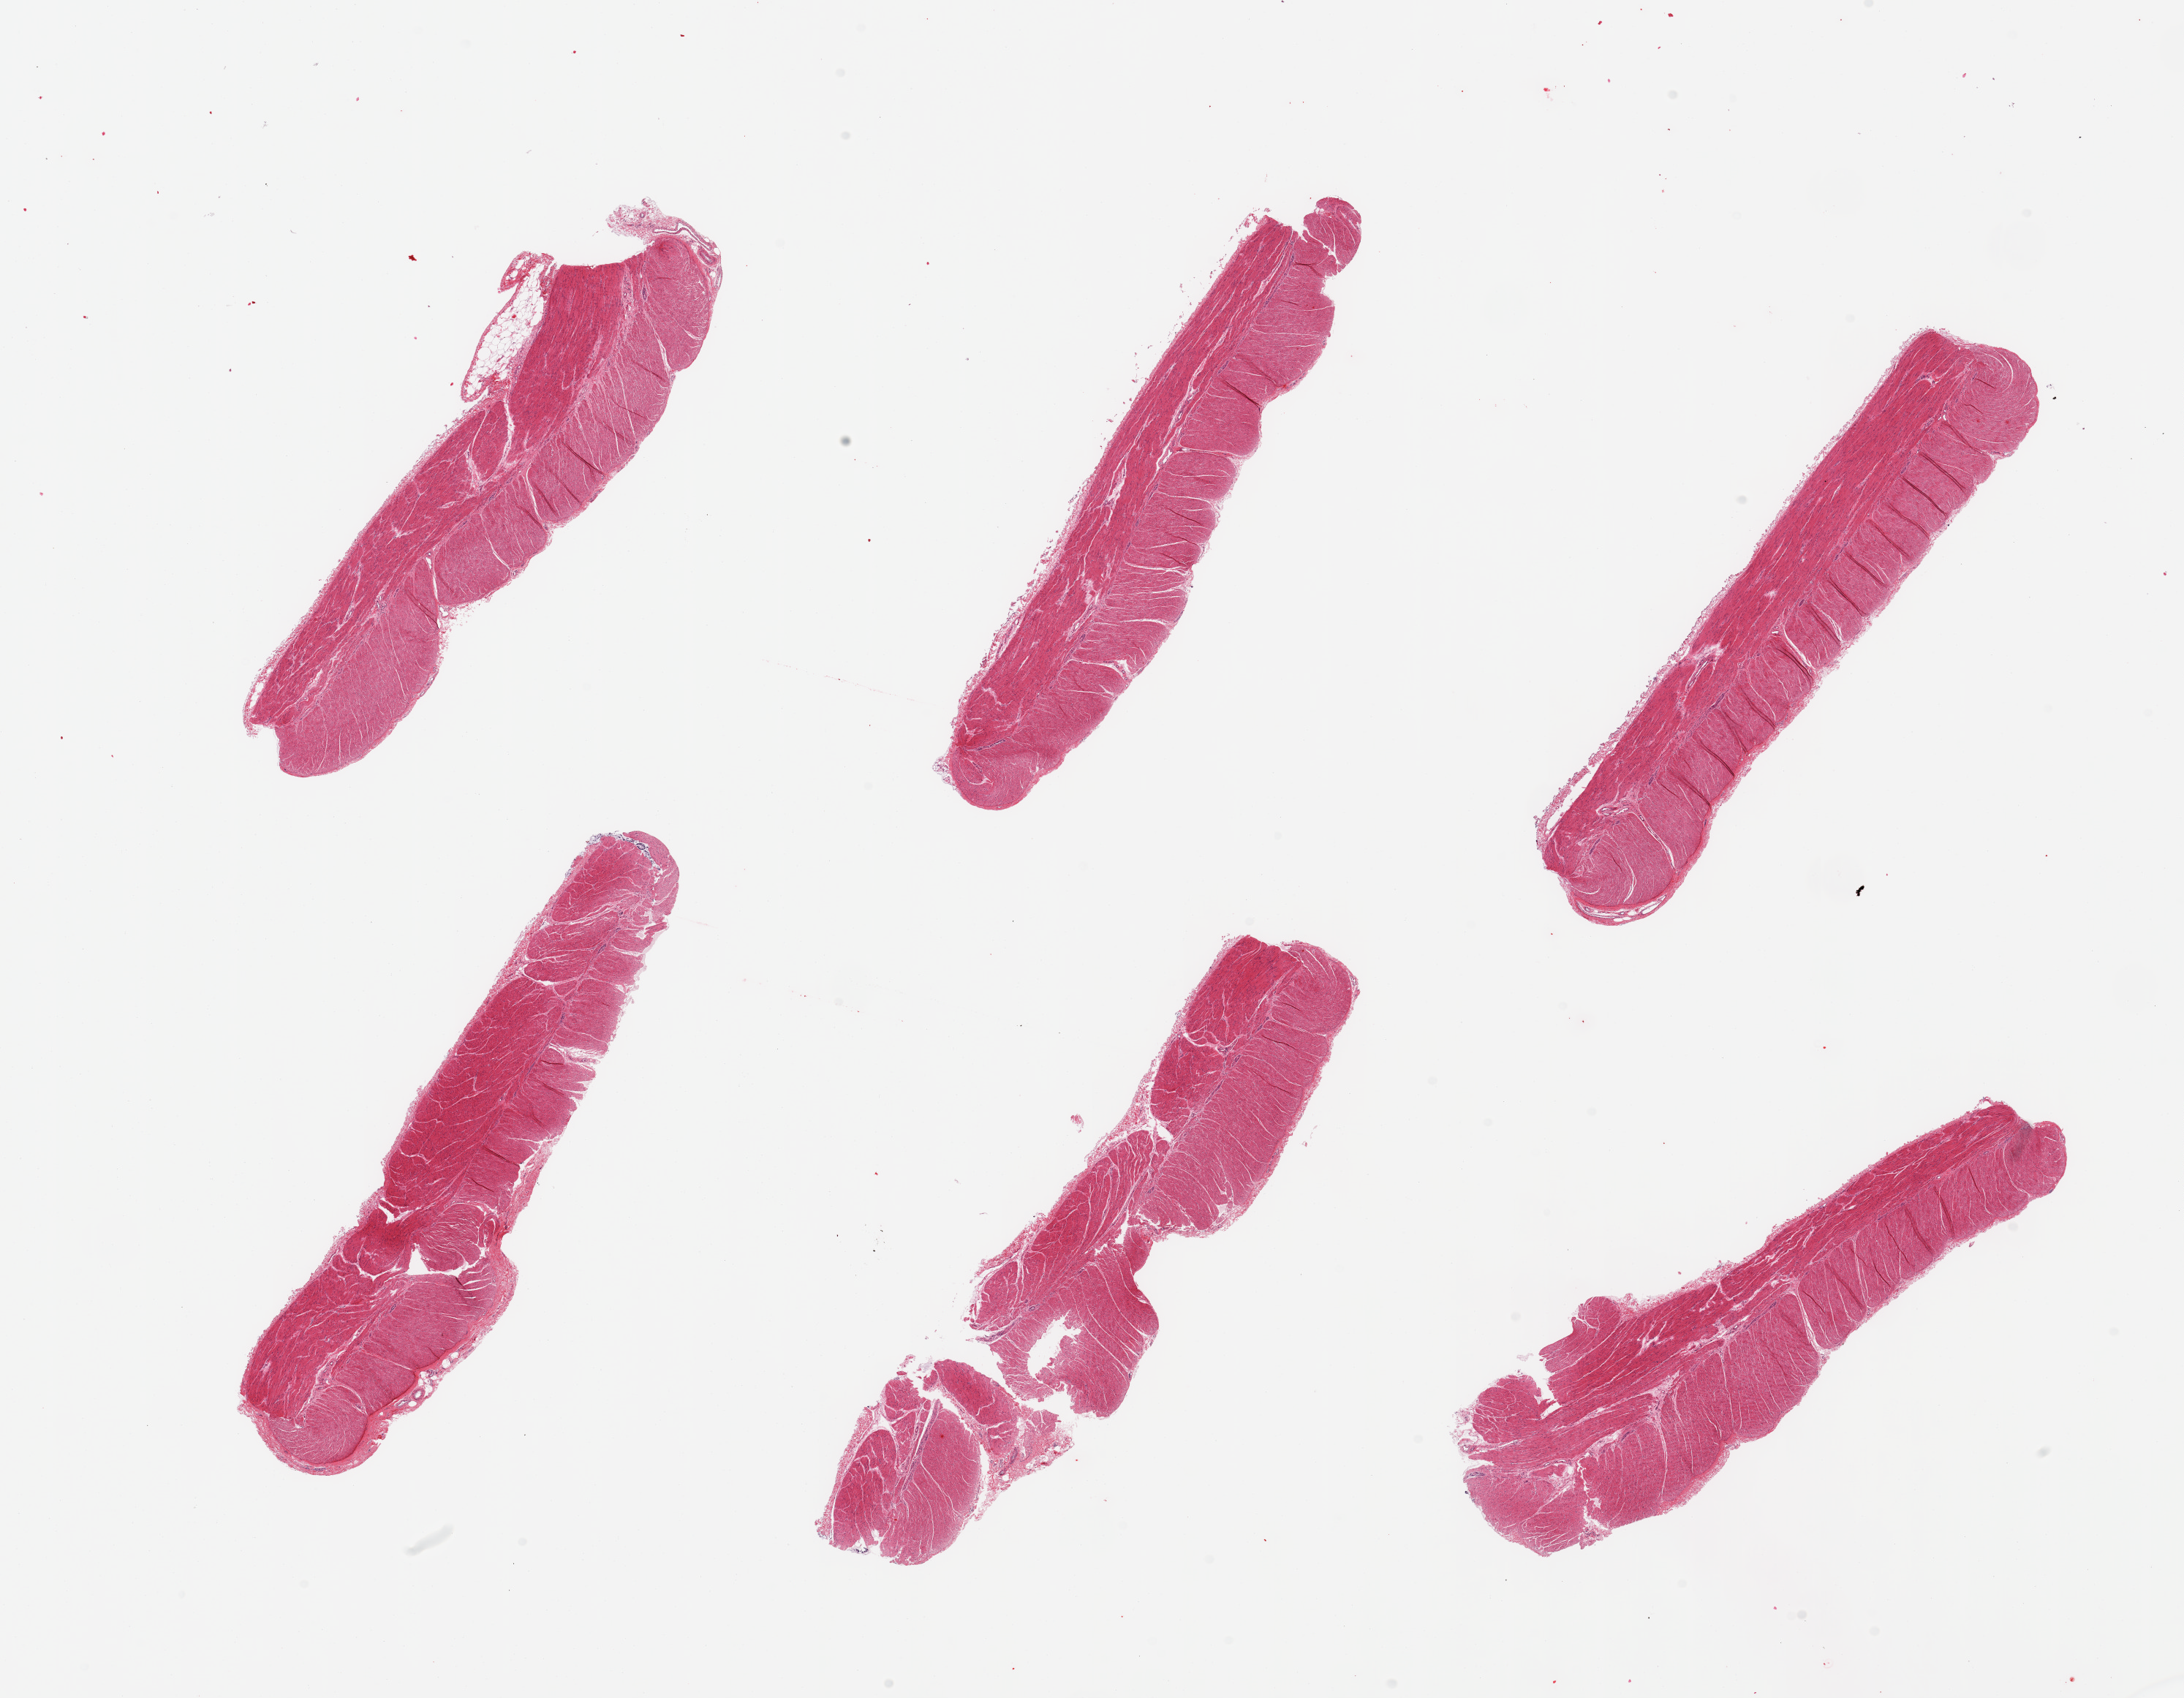
Whole-slide image, H&E stain — whole scanned area (about 23.6 x 18.4 mm) shown as a low-resolution overview. PAXgene-fixed paraffin-embedded (PFPE) section. Sampled site (target tissue): sigmoid colon. Donor tissue sample. Male donor.
Reviewer comment on this tissue sample: 6 pieces; target muscularis.